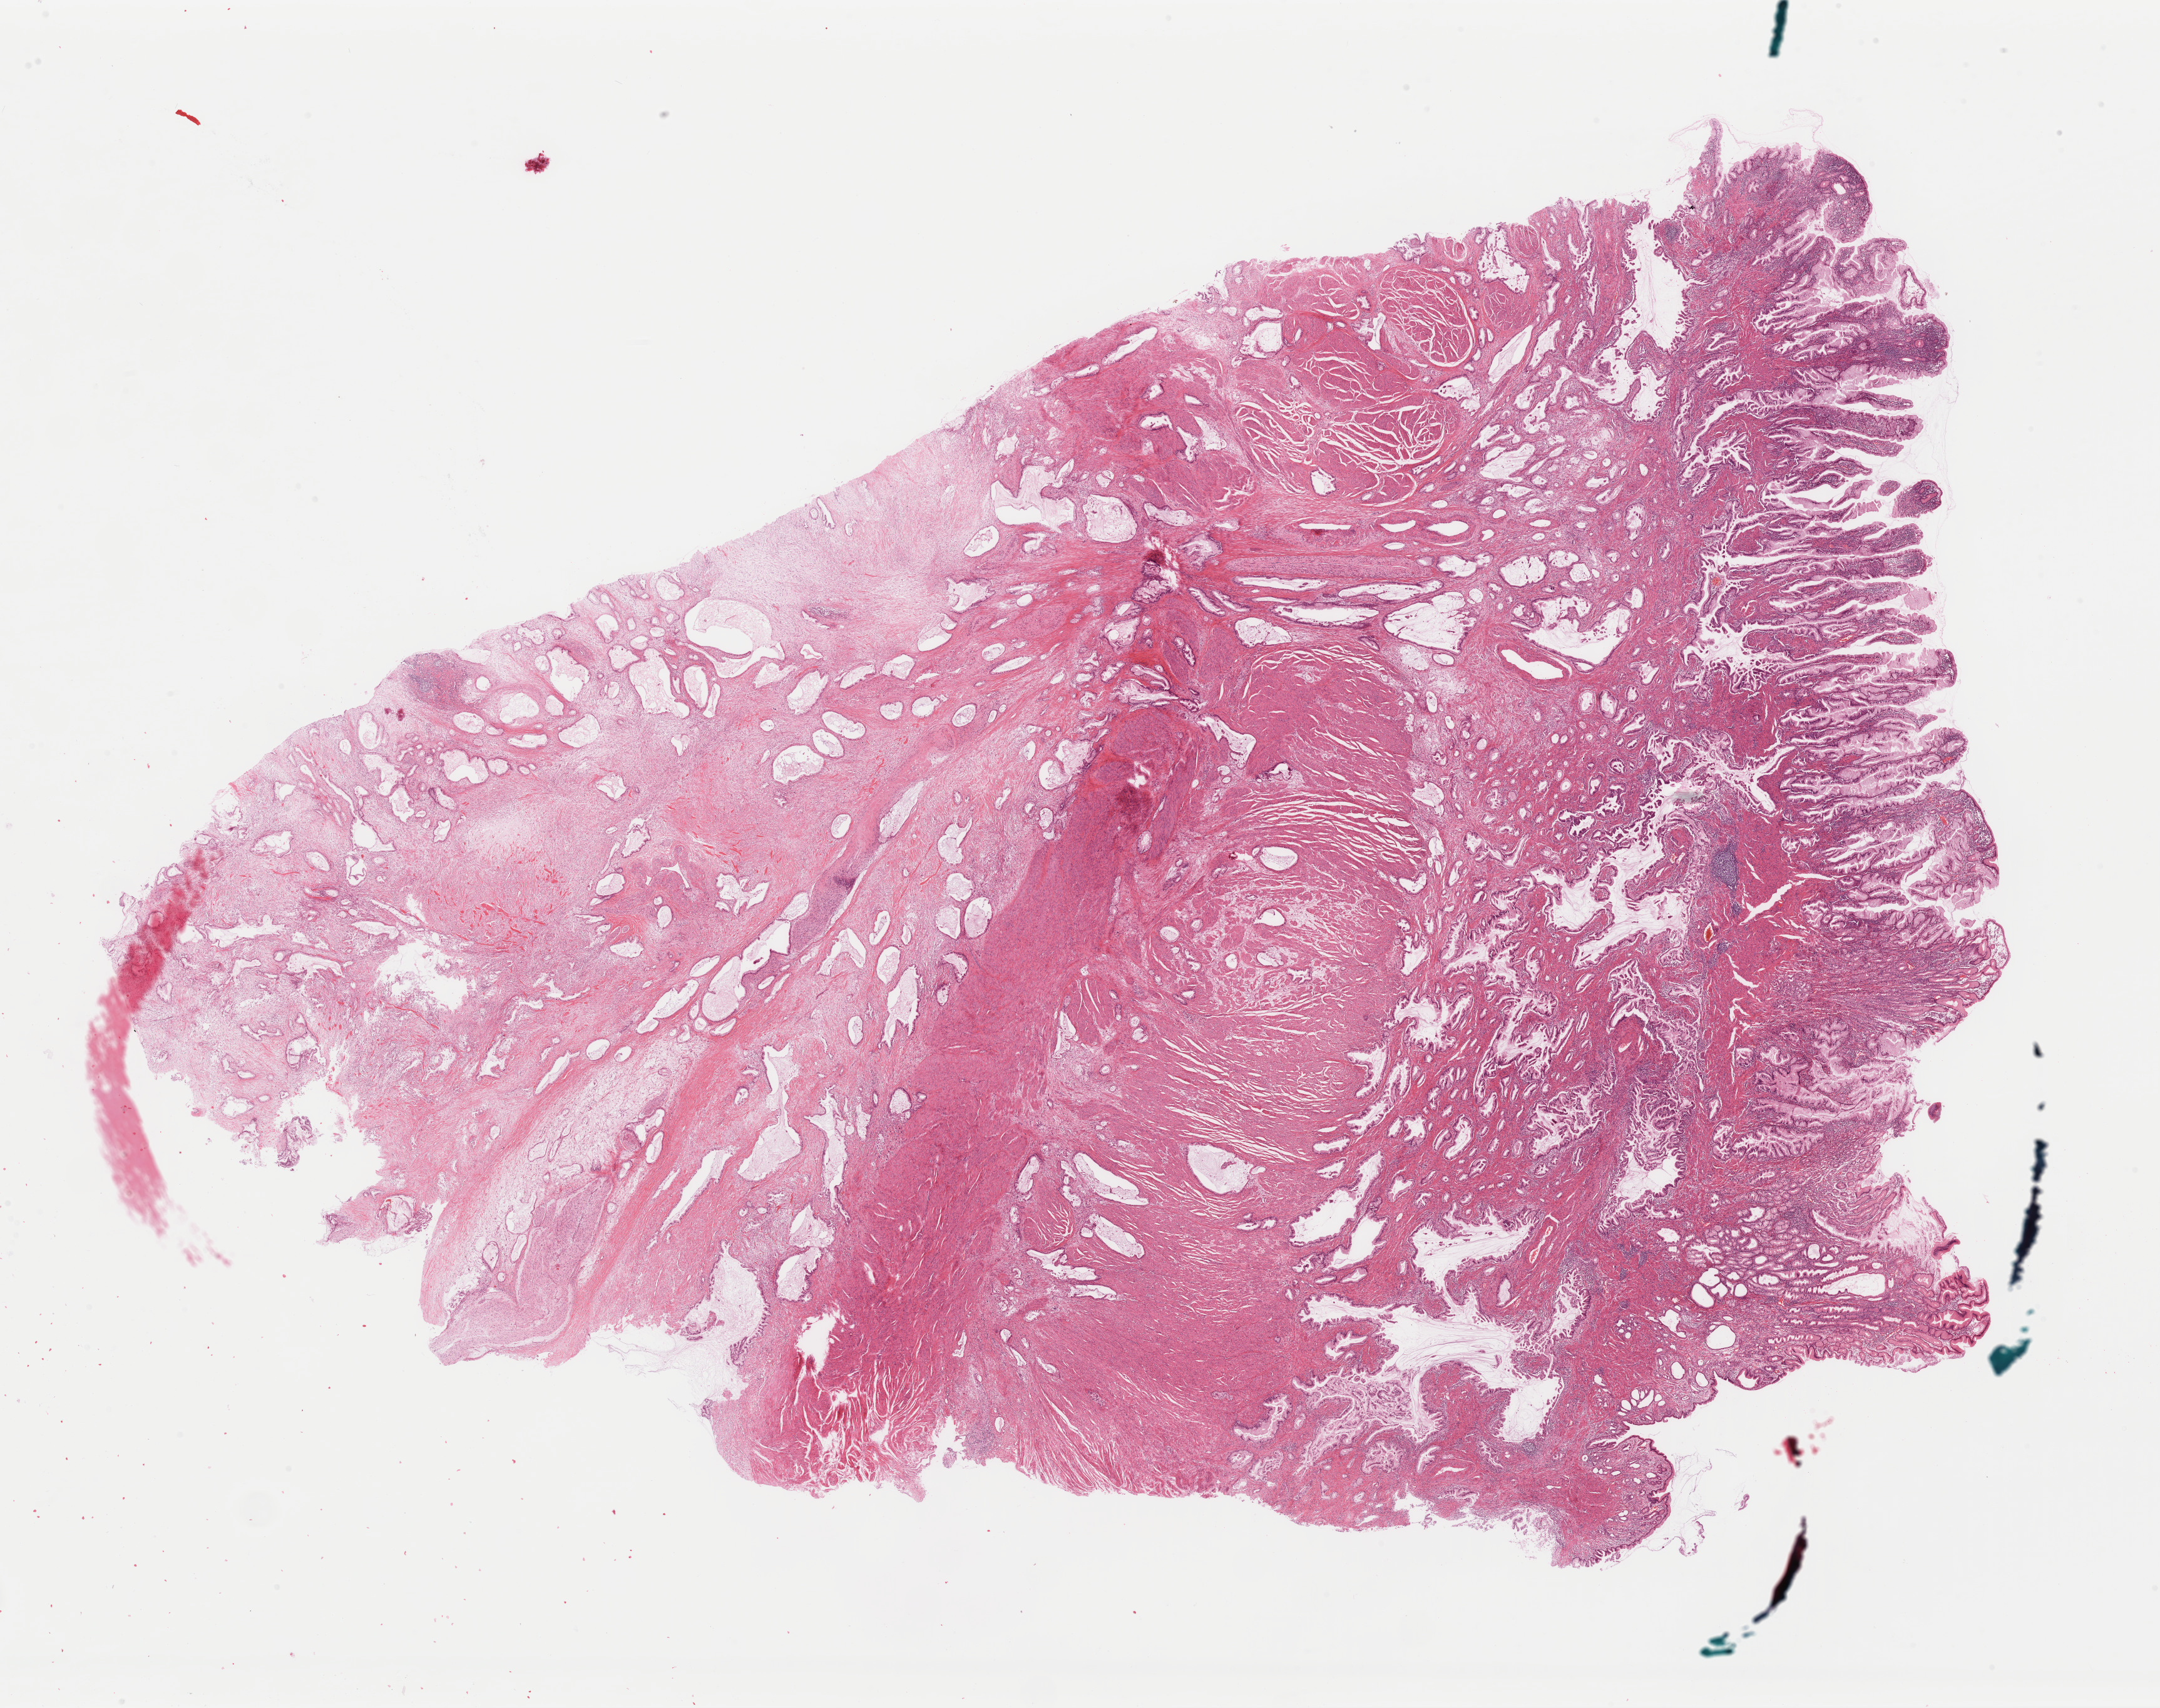
Hematoxylin and eosin (H&E) stained whole-slide image — a low-resolution overview of the entire scanned area, about 27.3 x 21.6 mm; FFPE section; stomach, primary tumour sample. Female patient; age at initial diagnosis 69 years. Histologic grade: G2 (moderately differentiated).
AJCC pathologic stage: IIA (7th edition). Histologic diagnosis: Adenocarcinoma, NOS (cardia, NOS). Lymph nodes positive (case pathology): 0 of 10 examined.